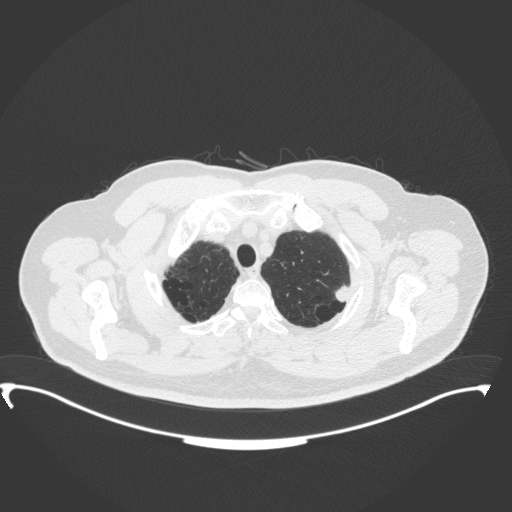
Chest CT, one axial slice. Slice 325 of 350 in the series (ordered by position). Reconstruction kernel B31f. 120 kVp. Lung window (W 1500 / L -600 HU). 1 mm slice thickness. 512 × 512 image matrix, field of view 459 × 459 mm. Male patient, age 64 years. From the clinical record (not read from this slice): clinical TNM (as recorded): T1c N1 M1.
Annotated regions visible in this slice (bounding box drawn by a radiologist):
- lung tumour (recorded histology: adenocarcinoma): box from (x=333, y=282) to (x=353, y=305) px